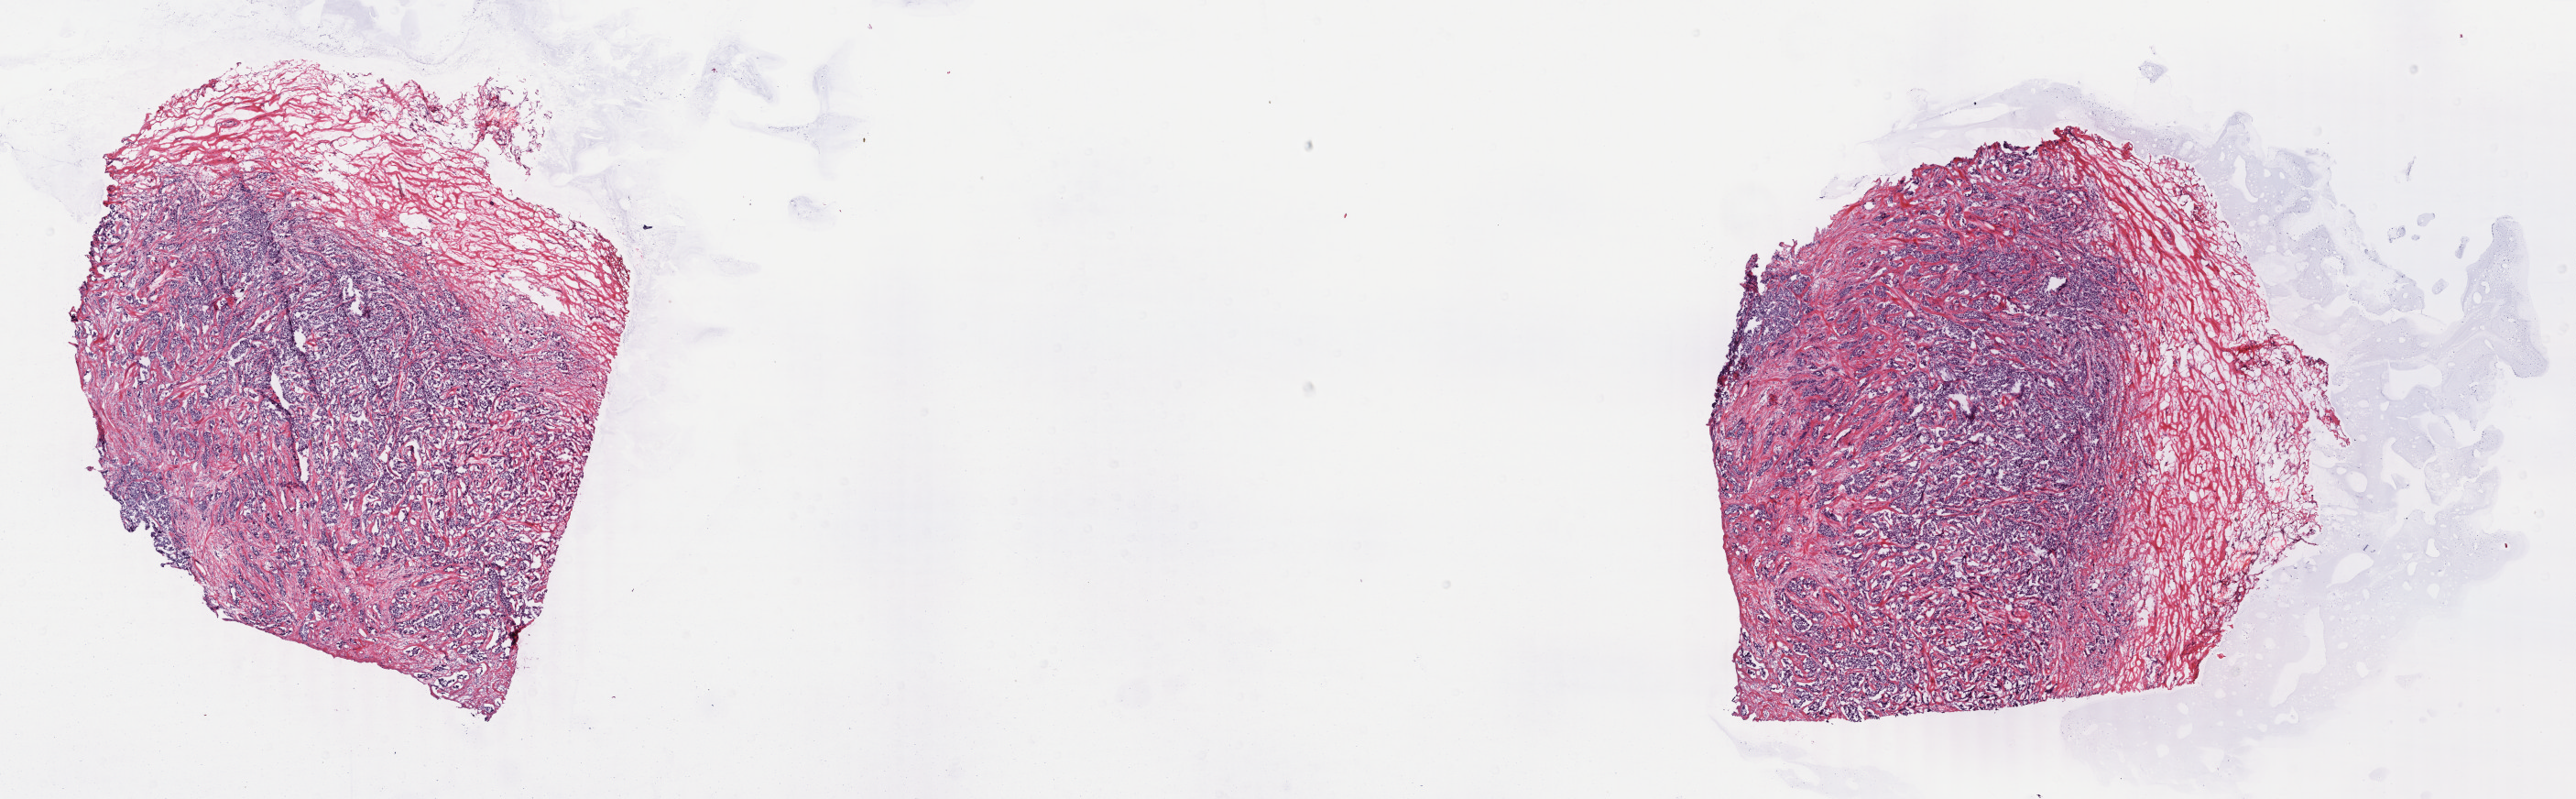
H&E-stained whole-slide image, shown as a low-resolution overview of the whole scanned area (about 22.4 x 6.9 mm), frozen section, breast, primary tumour sample. Female, age 62 years at initial diagnosis. Pathologist review of this section (percent, as recorded): tumour cells 85%, tumour nuclei 85%, normal cells 0%, stromal cells 15%, necrosis 0%. Infiltration values recorded for this section: lymphocyte infiltration 4%, monocyte infiltration 0%, neutrophil infiltration 0%.
Laterality: right. Lymph nodes positive (case pathology): 1 of 23 examined. Pathologic diagnosis: Infiltrating duct carcinoma, NOS. AJCC pathologic stage: IIB (6th edition).